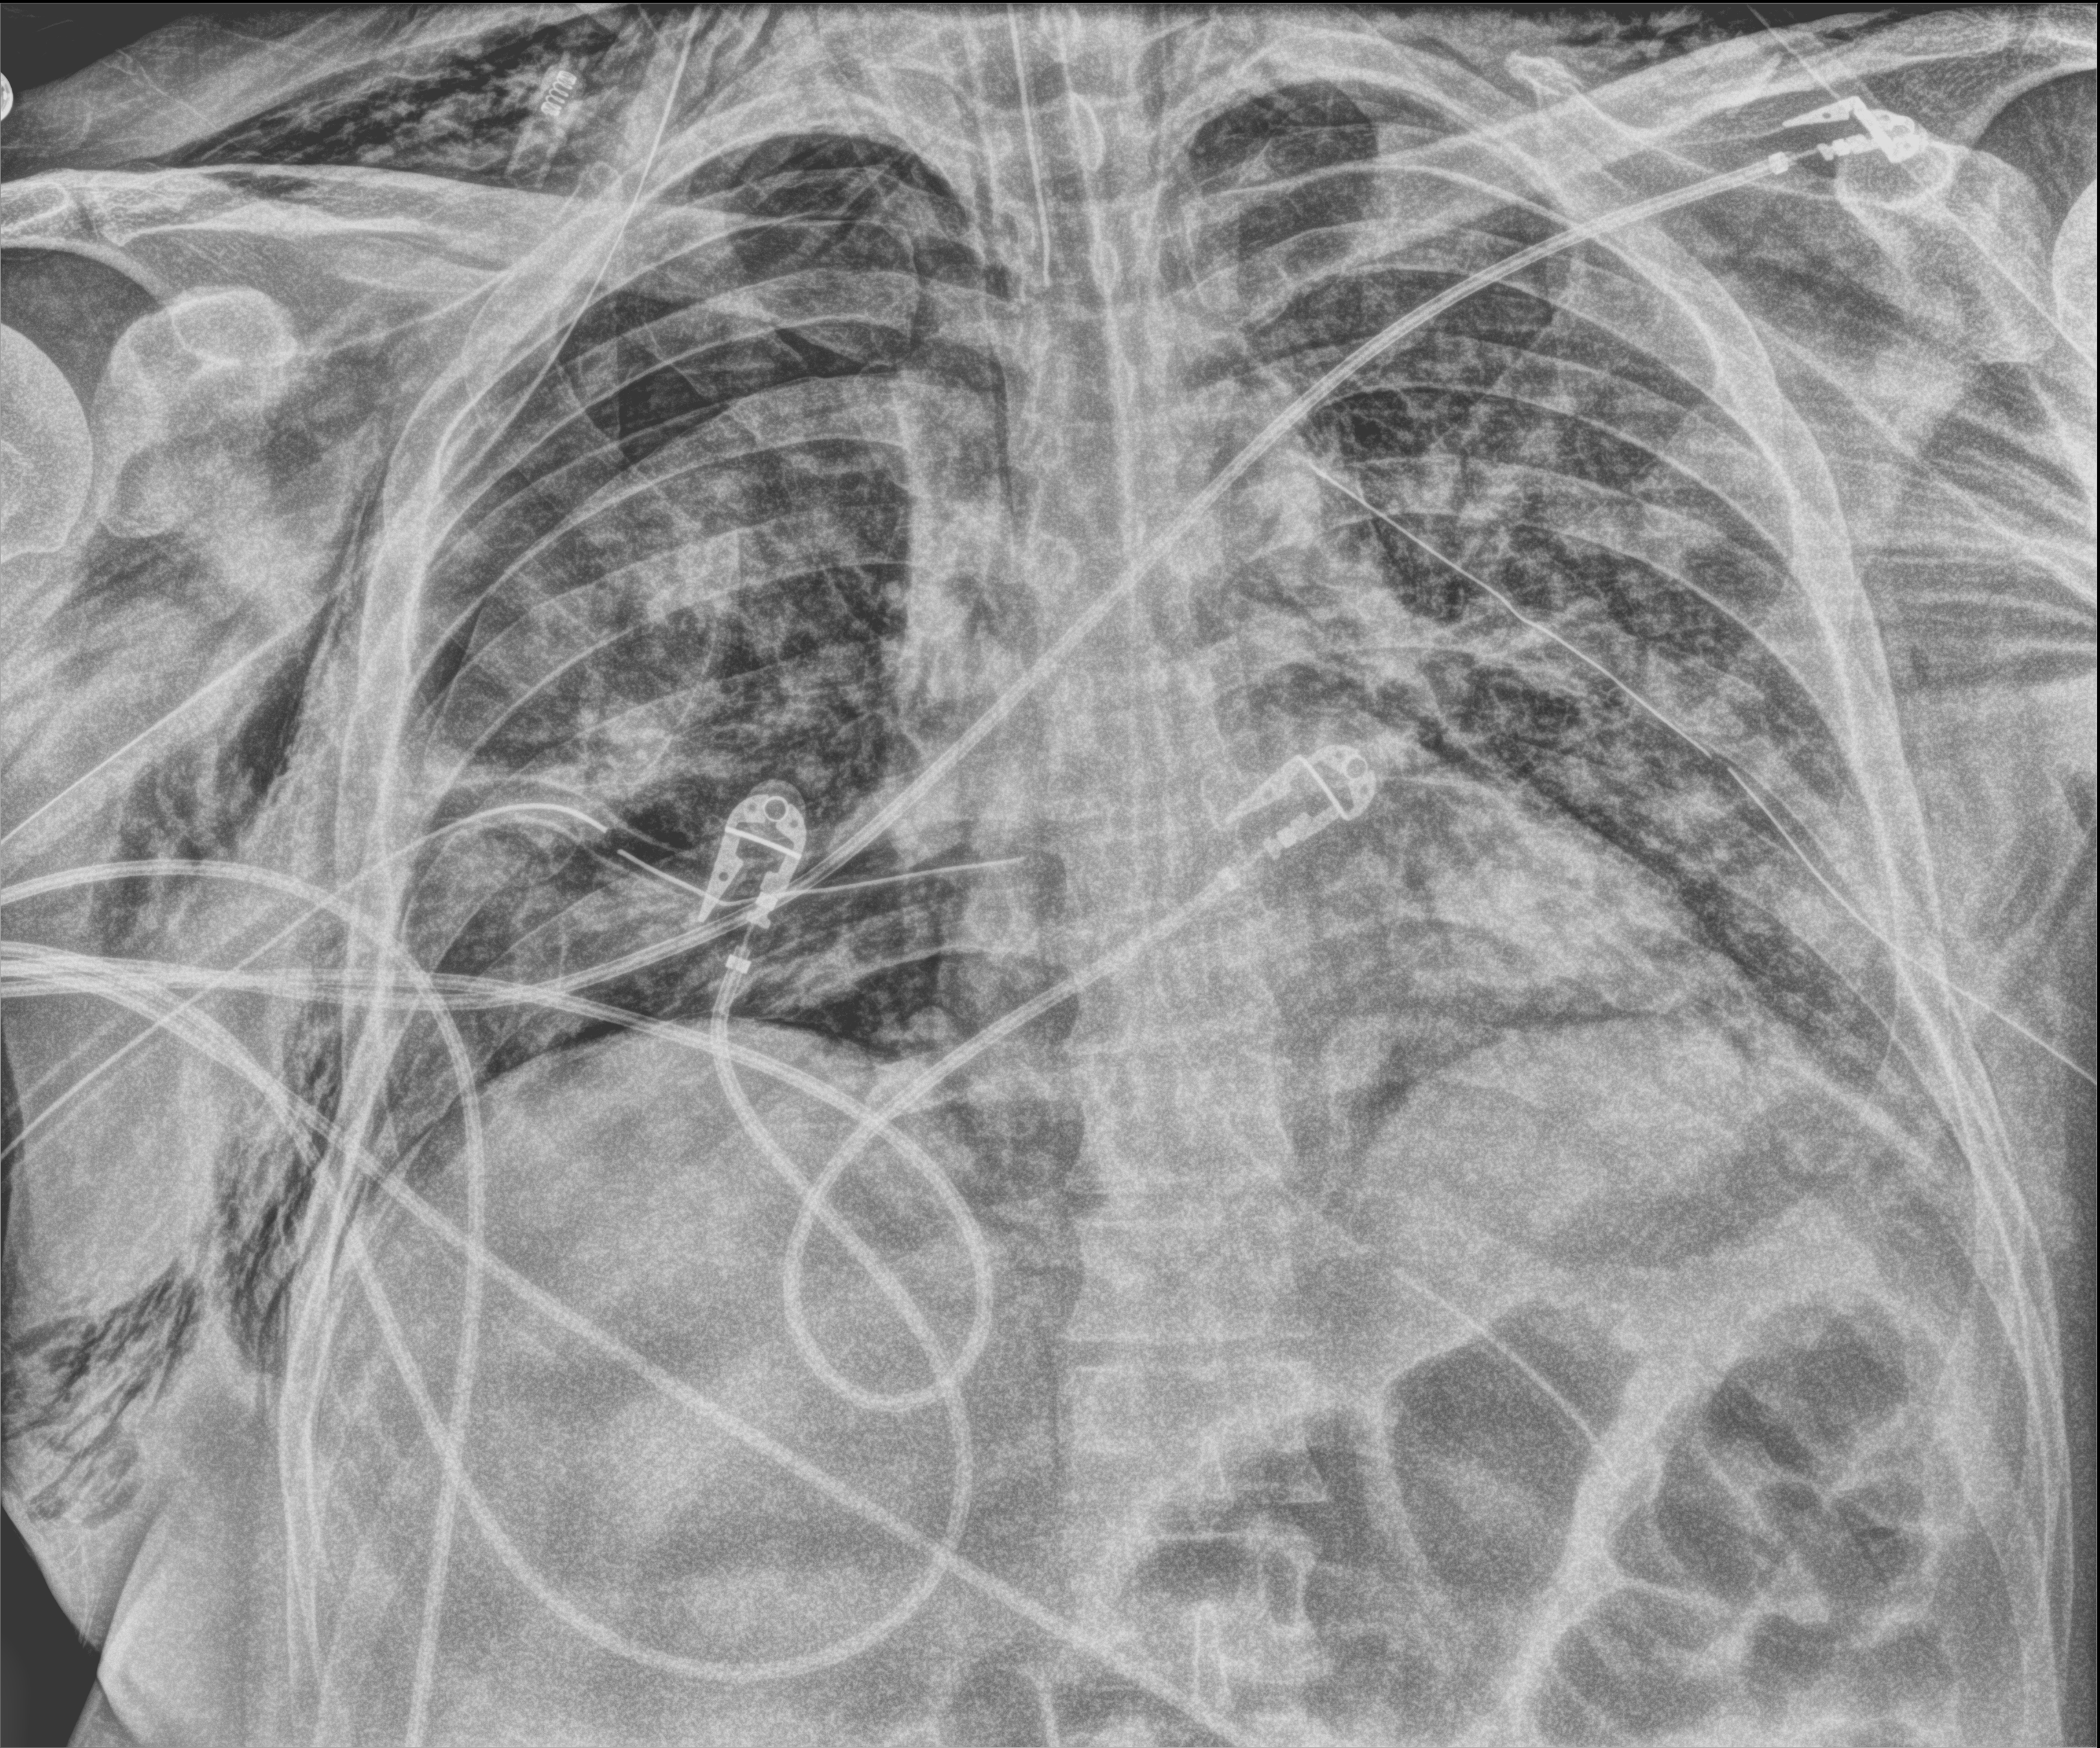
Chest X-ray (portable); anteroposterior (AP) projection. Male patient hospitalised with COVID-19, age 18–59 years.
Admission-level facts for this patient (not findings on this image; timing relative to this image not recorded): mechanically ventilated during this hospital stay: yes; chronic kidney disease (admission record): no.